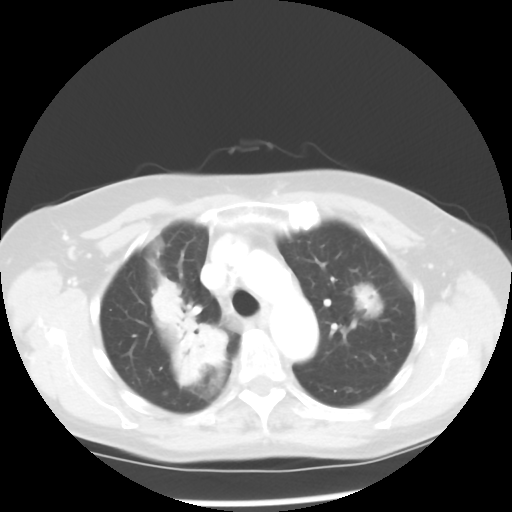
Chest CT, one axial slice. Slice 37 of 52 in the series (ordered by position). Lung window (W 1500 / L -600 HU). 5 mm slice thickness. 512 × 512 image matrix, field of view 328 × 328 mm. Patient: female, 60 years. From the clinical record (not read from this slice): clinical TNM (as recorded): T2 N1 M1a.
Structures marked on this image (bounding box drawn by a radiologist):
- lung tumour (recorded histology: adenocarcinoma): bounding box (x1, y1, x2, y2) in pixels: (151, 274, 228, 388)